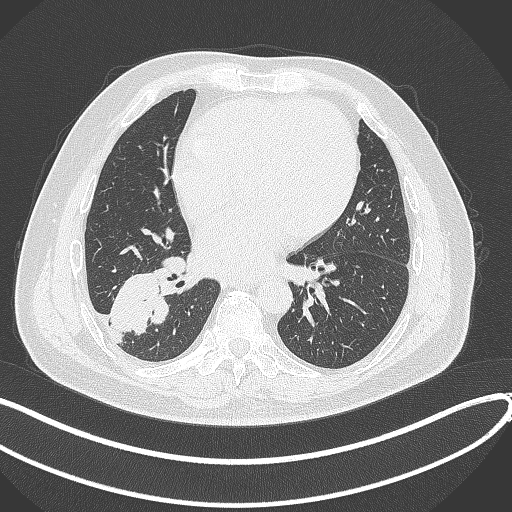
Chest CT, one axial slice. Slice 153 of 360 in the series (ordered by position). 120 kVp. Lung window (W 1500 / L -600 HU). 1 mm slice thickness. 512 × 512 image matrix. Patient: male, 59 years.
Annotated regions visible in this slice (rectangle marked by the reading radiologist):
- lung tumour (recorded histology: adenocarcinoma): bounding box (x1, y1, x2, y2) in pixels: (109, 267, 172, 337)